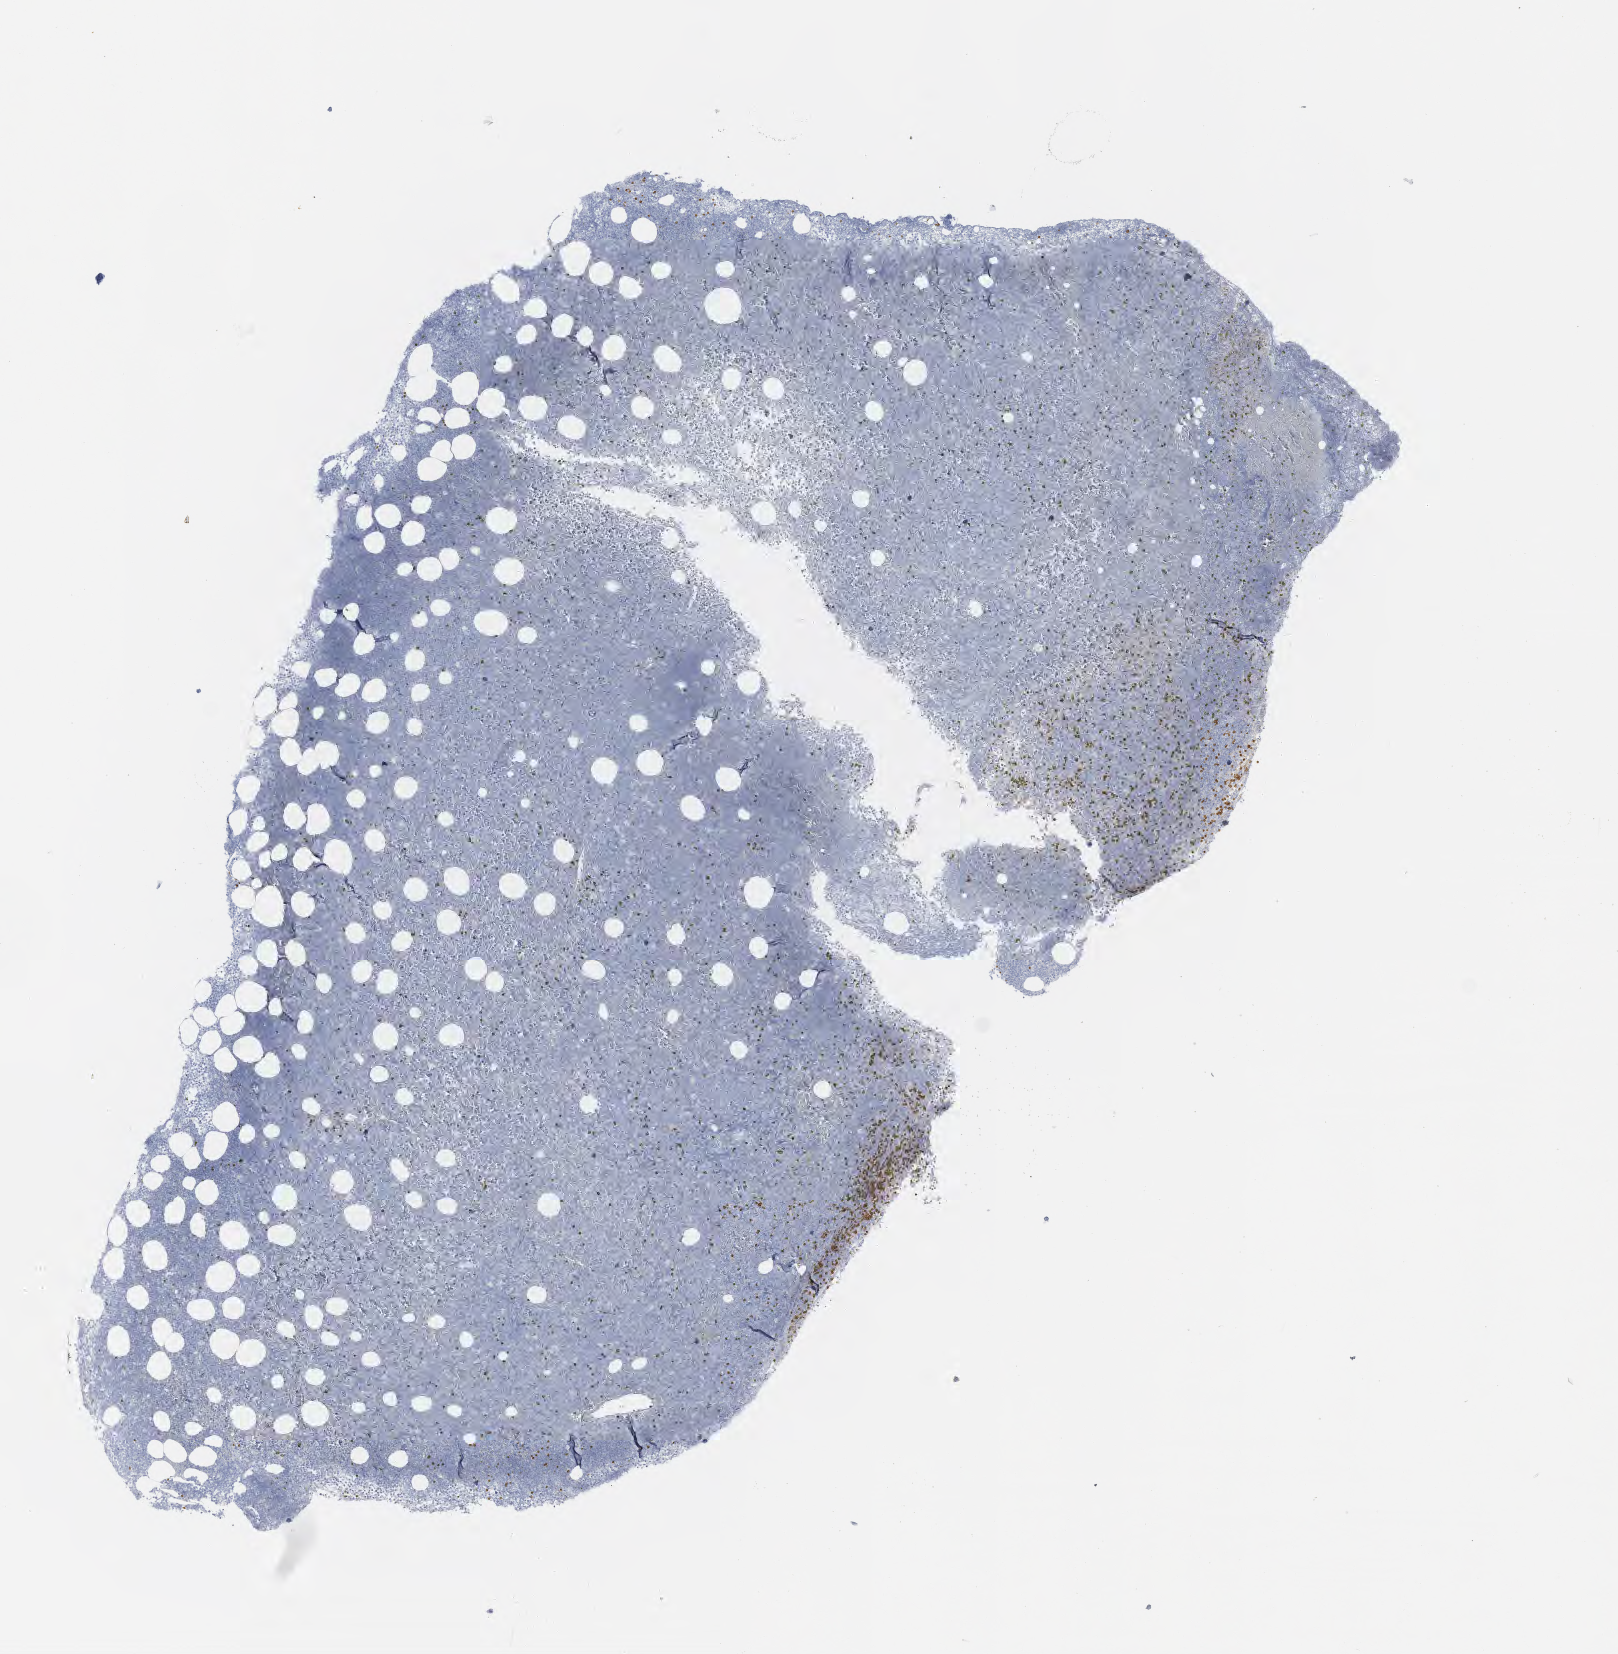
Immunohistochemistry (IHC) whole-slide image stained for CD3 — low-resolution overview of the scanned area, about 6.5 x 6.7 mm; tumor tissue; anatomic site: bone marrow. Patient: male, age 70 years.
* diagnosis: Neoplasm, uncertain whether benign or malignant